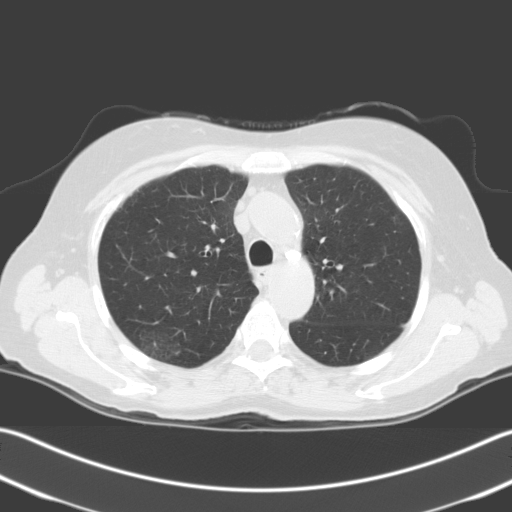
Axial slice from a low-dose chest CT screening exam, first (baseline) screen, lung window (W 1500 / L -600 HU), slice 48 of 204 in the series. Female, age 67 years at enrolment.
Lesion marked by an expert reader, bounding box <126,323,191,373> (left, top, right, bottom; pixels). The screening reader recorded 2 non-calcified nodules or masses ≥4 mm on this exam (right upper lobe, right upper lobe); which of them this box marks is not recorded. Lung cancer was diagnosed 24 days after this screen: squamous cell carcinoma, NOS, right upper lobe, stage IIIA (AJCC 6th edition), 56 mm at pathology.